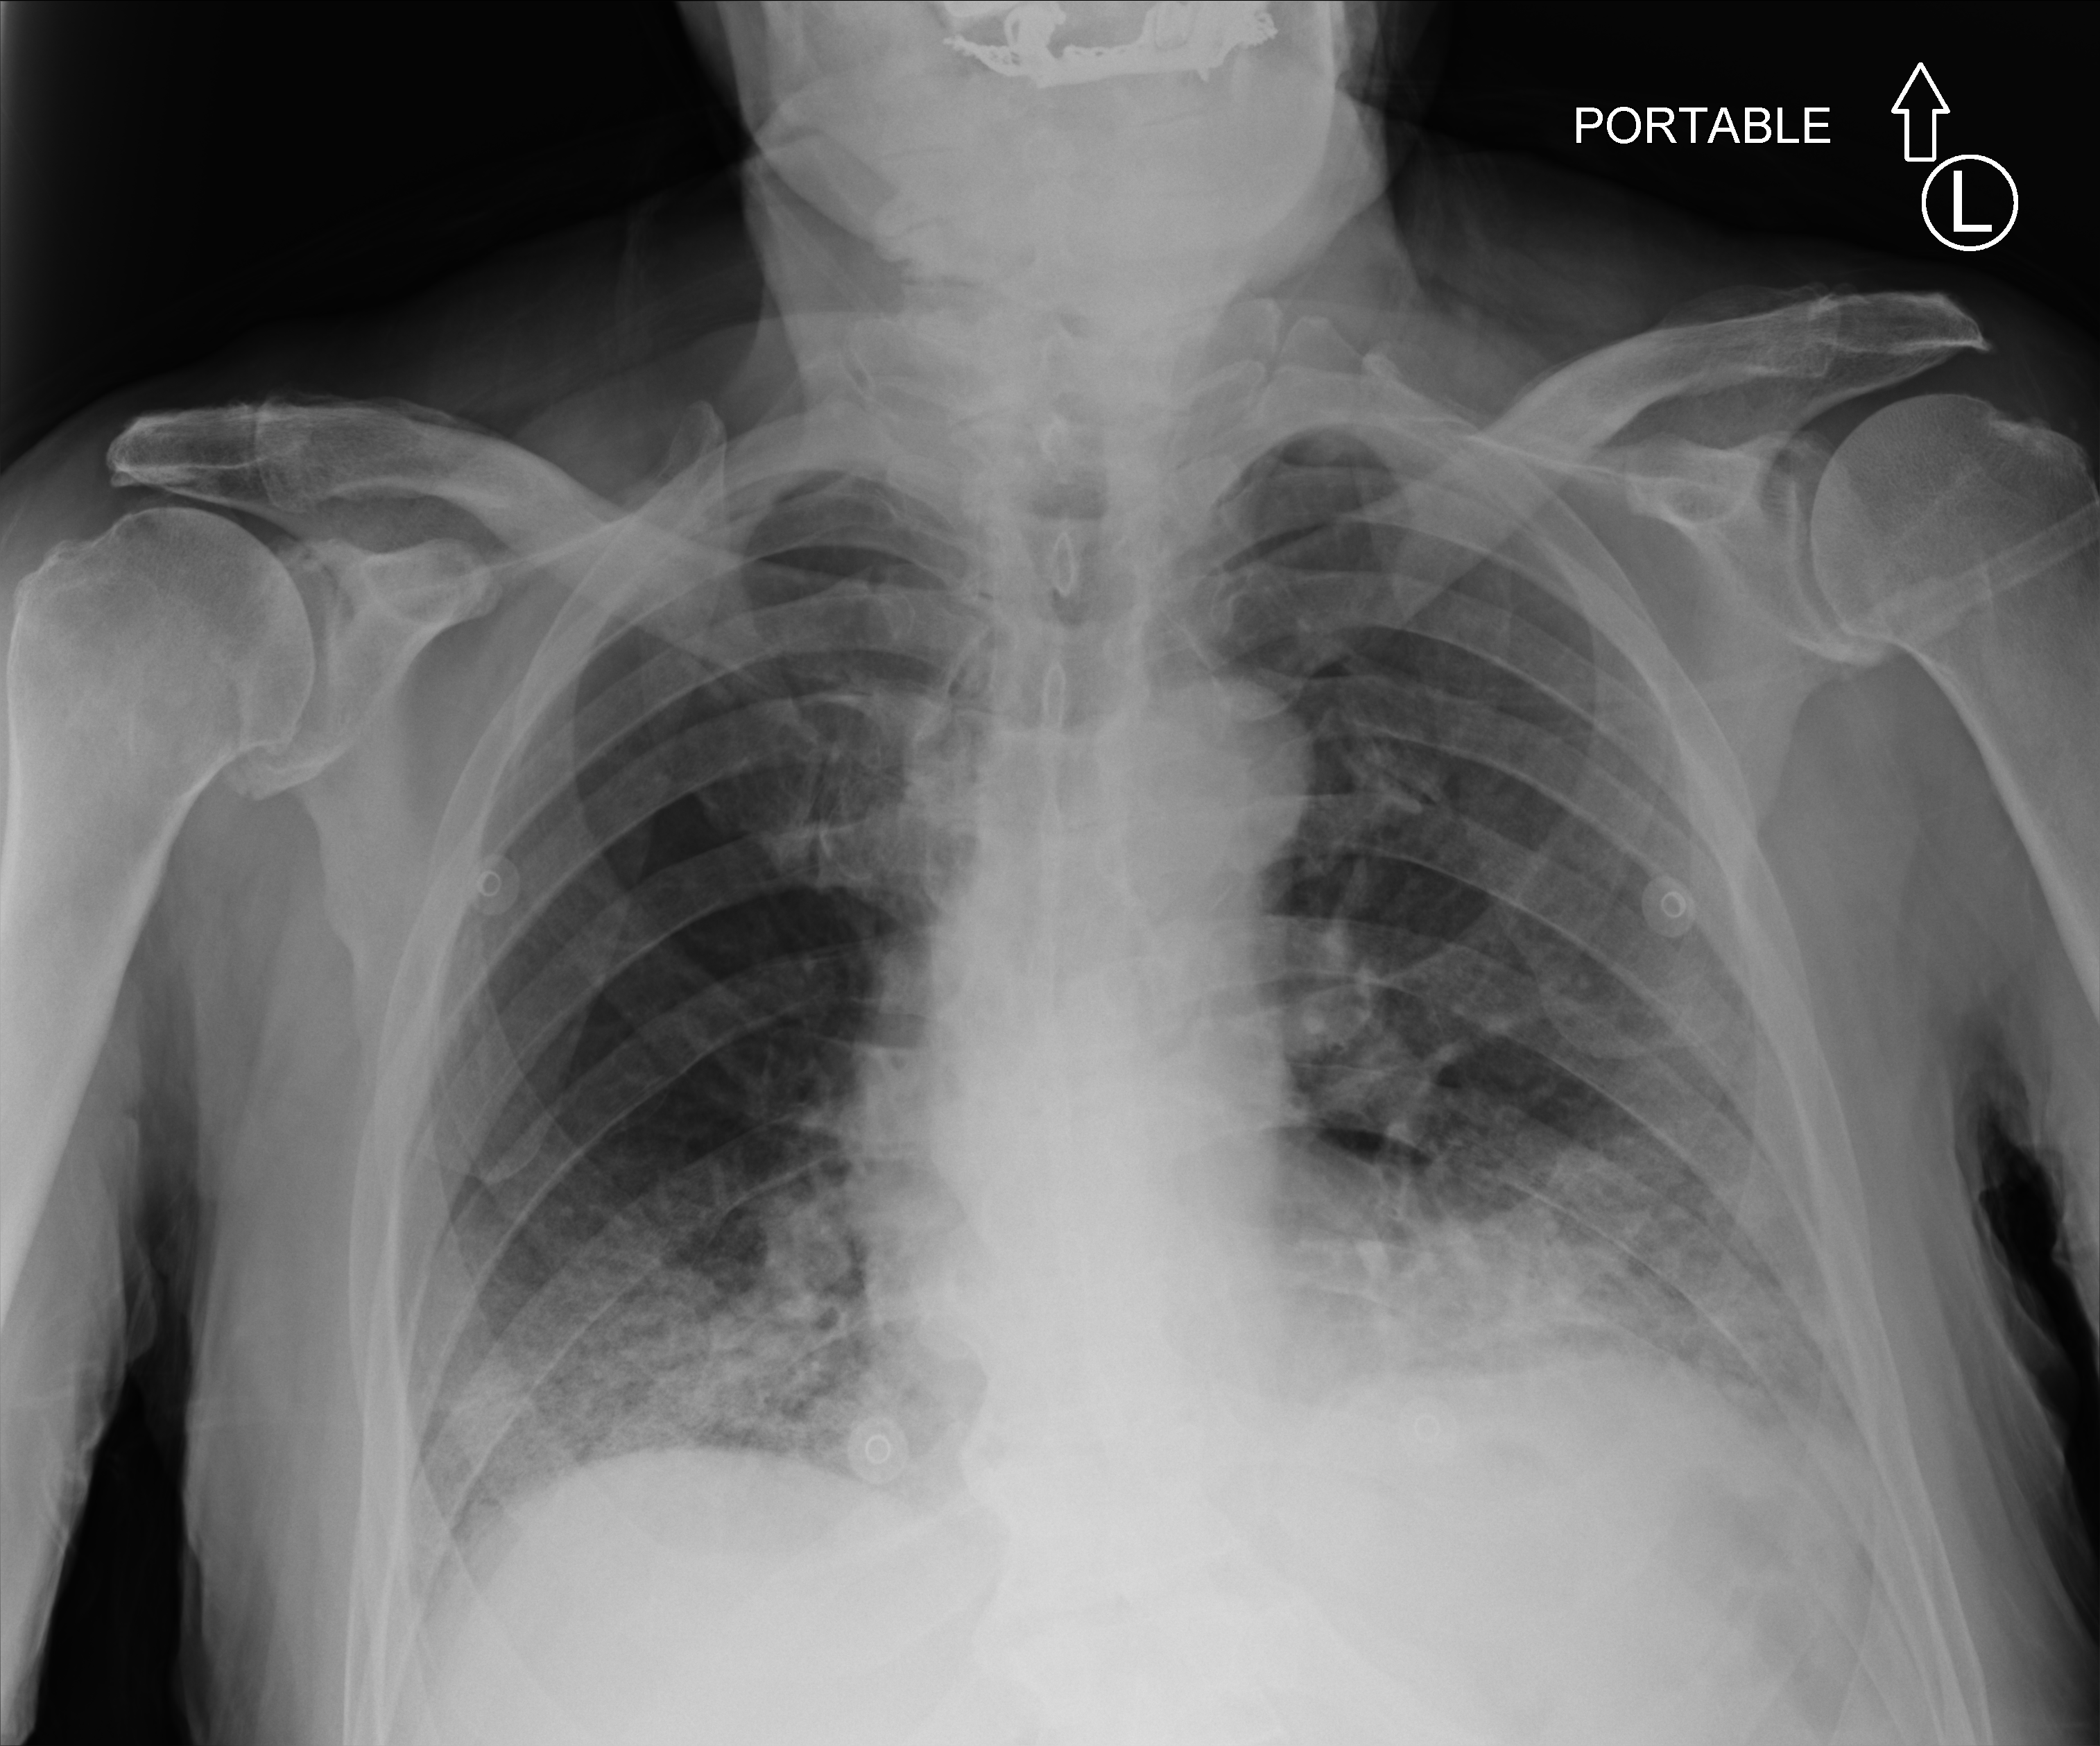
Chest X-ray (portable). Patient hospitalised with COVID-19; male, aged 75–90 years.
Admission-level facts for this patient (not findings on this image; timing relative to this image not recorded): admitted to intensive care during this hospital stay: yes; mechanically ventilated during this hospital stay: no.